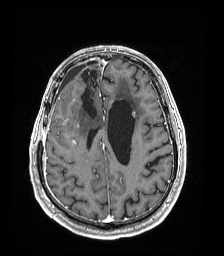
Brain MRI from a brain-tumour surgery series, one axial slice. Slice 63 of 192 in the series (ordered by position). T1-weighted post-contrast. 1 mm slice thickness. 224 × 256 image matrix. From the clinical record (not read from this slice): histopathology: Astrocytoma; WHO grade: 4; IDH mutation: yes.
Outlined on this slice (outlined manually by an expert reader):
- previous resection cavity: box from (x=81, y=68) to (x=98, y=118) px
- tumour: (x=72, y=139)–(x=76, y=145)